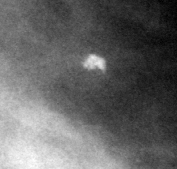
Crop from a digitized film mammogram around one marked abnormality; left breast; MLO view; BI-RADS breast density category 3 (scale 1–4).
- Calcifications, morphology round and regular / eggshell; BI-RADS assessment category 2; subtlety rating 3 on a 1 (subtle) to 5 (obvious) scale; benign; no additional work-up was recommended (benign without callback).